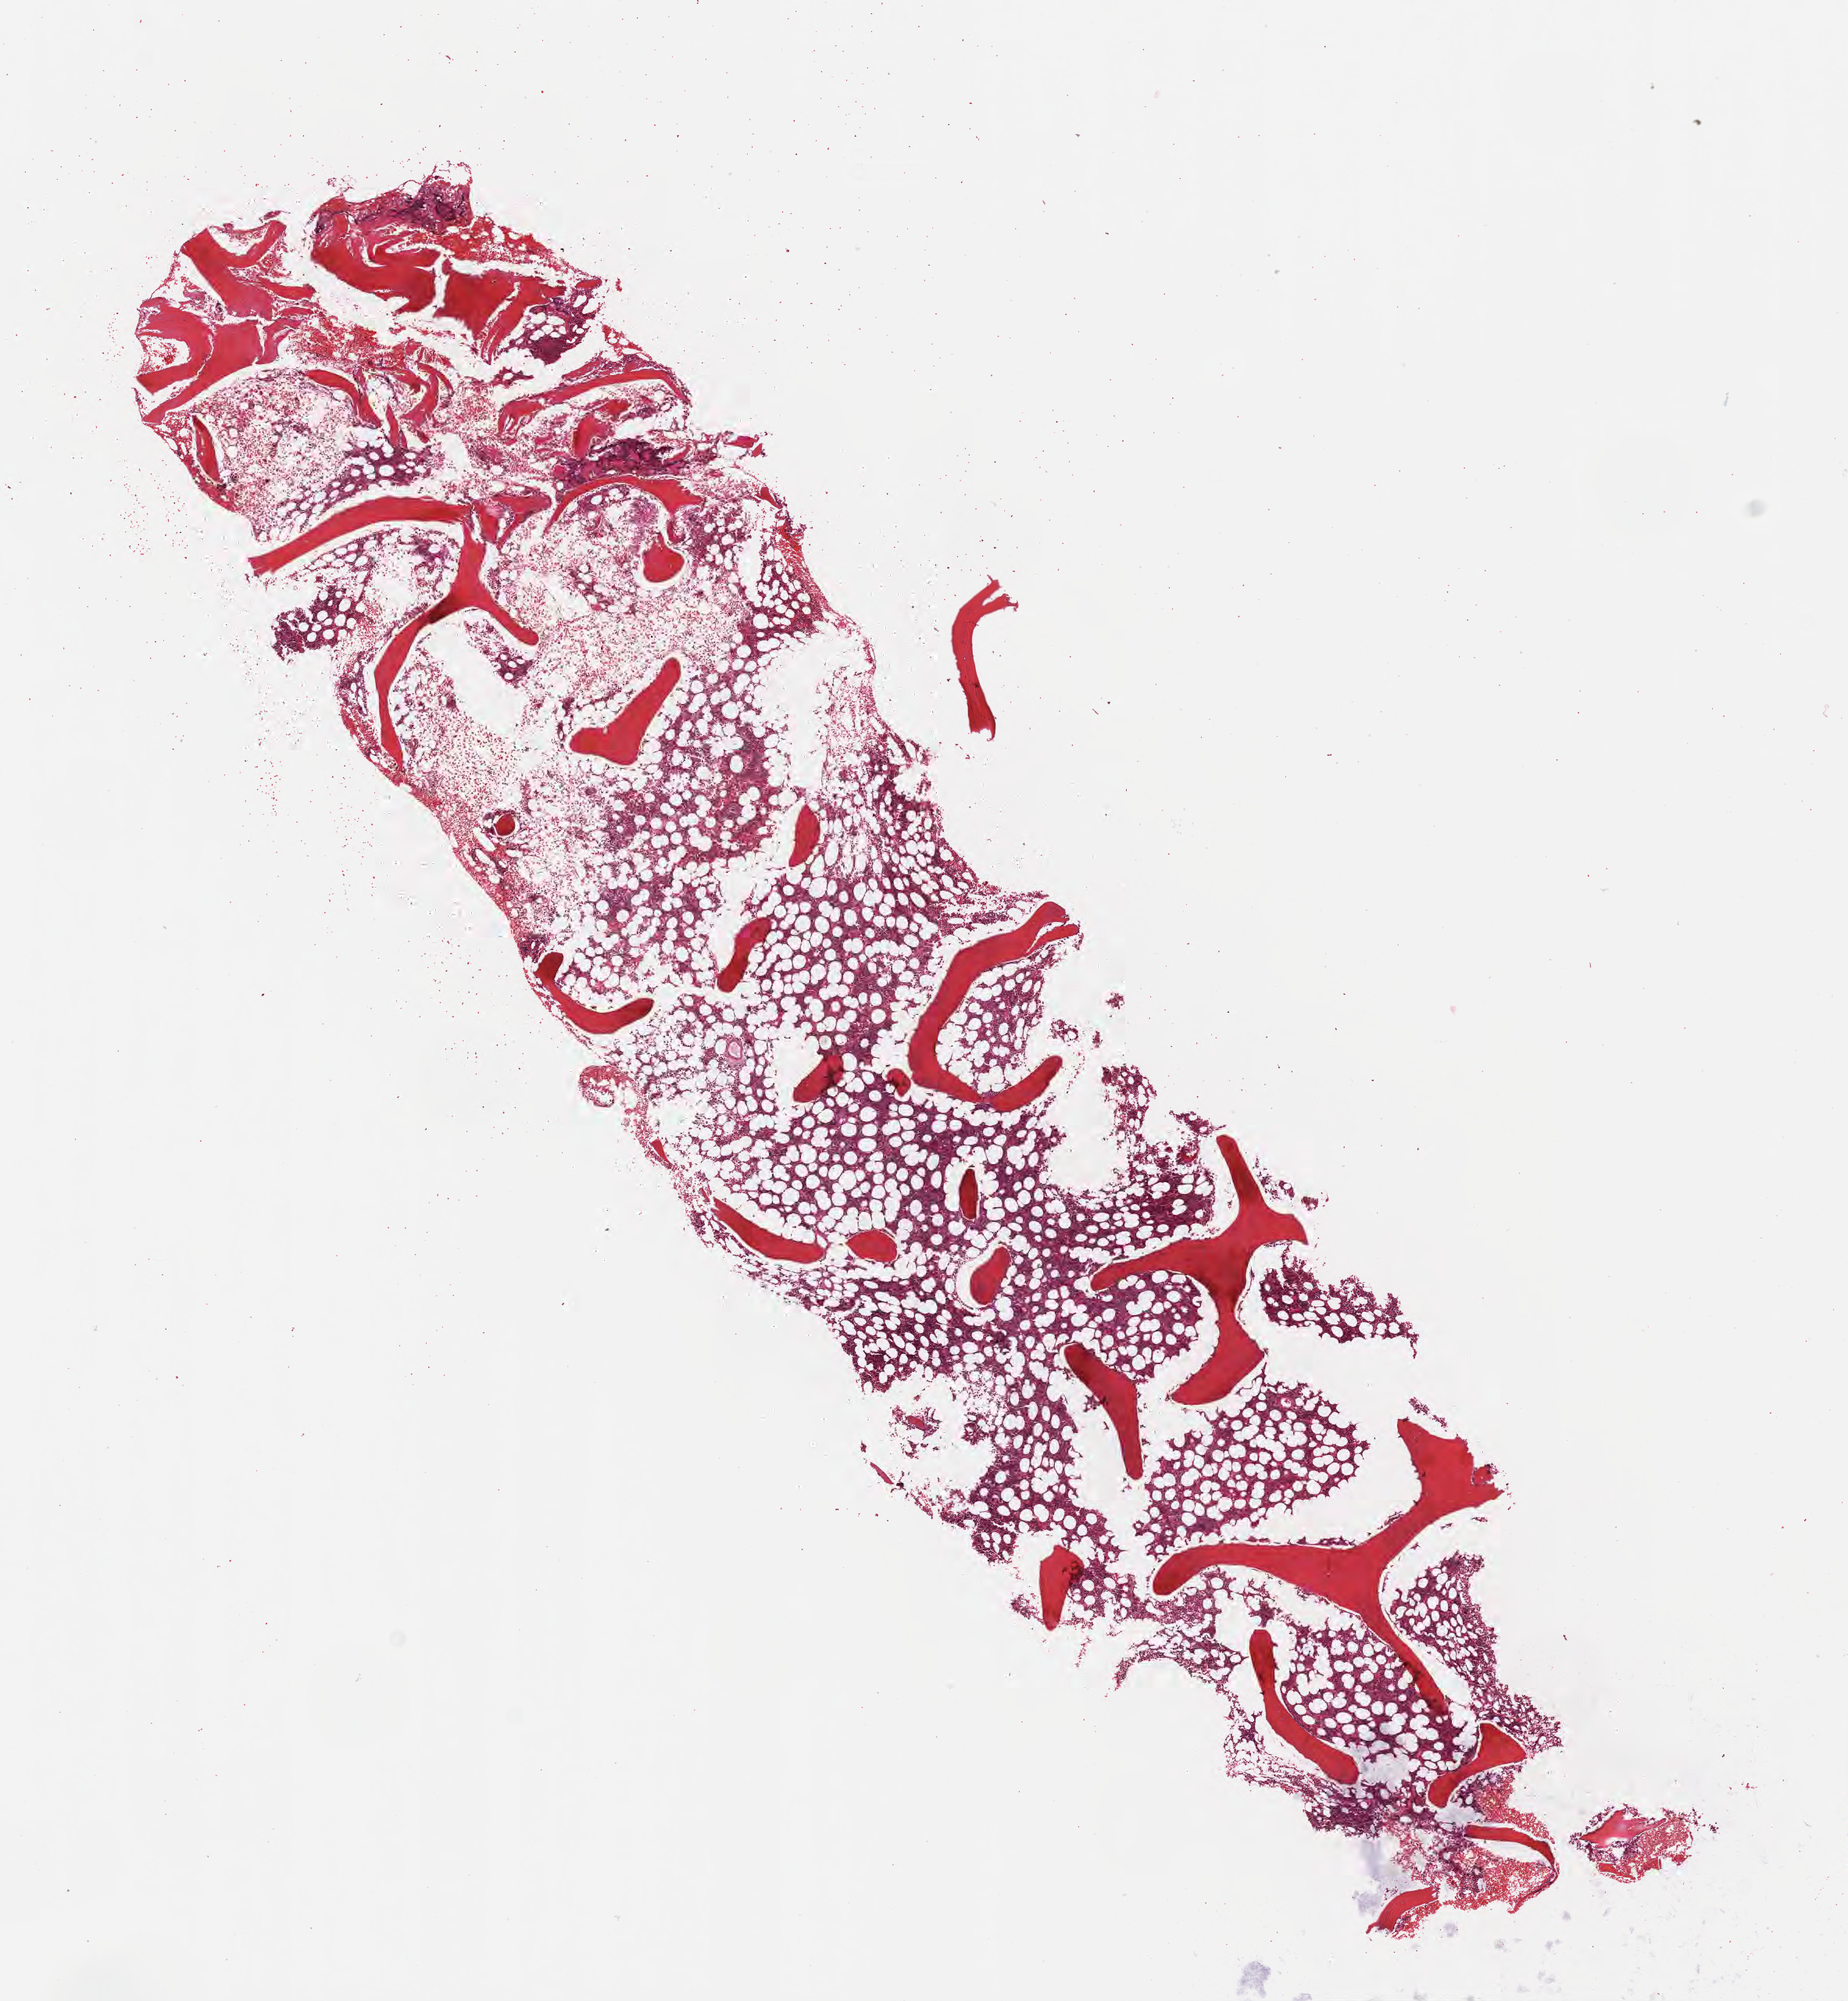
Hematoxylin and eosin (H&E) whole-slide image — a low-resolution overview of the entire scanned area, about 9.6 x 10.3 mm. Formalin-fixed paraffin-embedded section. Normal-tissue sample (non-tumor) from a patient with burkitt lymphoma, NOS. Patient male; age 40 years. Composition of this section per pathologist review: tumor cells 0%, tumor nuclei 0%, stromal cells 0%, necrosis 0%, normal cells 100%. Inflammatory infiltration, as recorded: lymphocyte infiltration 20%, monocyte infiltration 10%, neutrophil infiltration 50%.
This section: non-tumor tissue sample; the patient's diagnosis is given above. Section: bottom of the tissue portion.